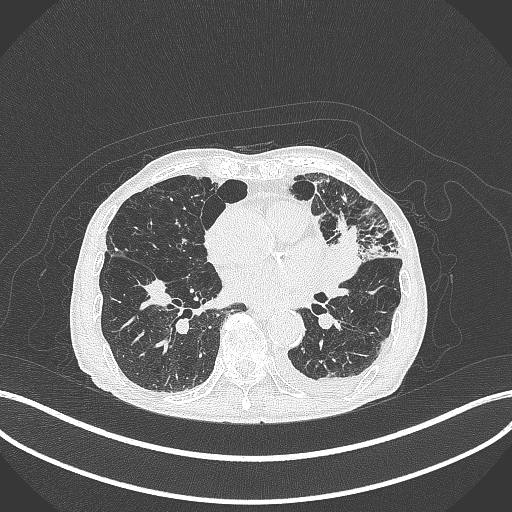
Chest CT, one axial slice; position 166 of 385 along the scan axis; reconstruction kernel B70f; 120 kVp; lung window (W 1500 / L -600 HU); 512 × 512 image matrix. Male patient, age 90 years or older. Case-level facts recorded for this patient, not image findings: clinical TNM (as recorded): T2b N1 M0.
Annotated regions visible in this slice (bounding box drawn by a radiologist):
- lung tumour (recorded histology: squamous cell carcinoma): box from (x=328, y=224) to (x=373, y=281) px